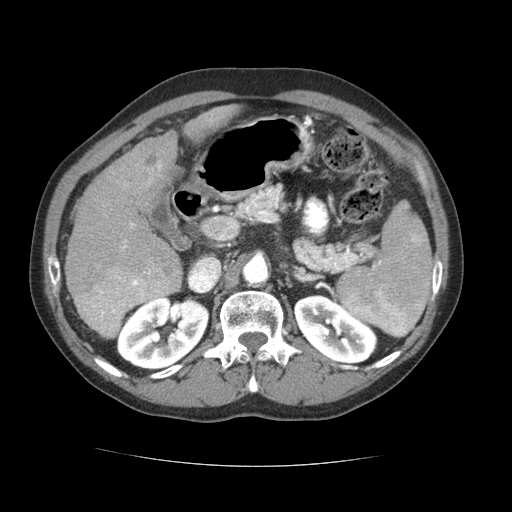
Contrast-enhanced abdominal CT (liver protocol), one axial slice. Position 38 of 69 along the scan axis. Reconstruction kernel STANDARD. 120 kVp. Soft-tissue window (W 400 / L 40 HU). 512 × 512 image matrix, field of view 360 × 360 mm. From the clinical record (not read from this slice): diagnosis: hepatocellular carcinoma (patient treated with transarterial chemoembolisation; whether this scan precedes or follows treatment is not stated here); TNM stage (as recorded): Stage-II; Child-Pugh class: B; tumour differentiation: poorly differentiated; tumour nodularity: multinodular.
Outlined on this slice (semi-automatically segmented with operator editing):
- liver parenchyma outside the tumour (the mass and vessels are separate outlines, so this box may not span the whole liver): bounding box [x1, y1, x2, y2] px = [64, 104, 240, 332]
- mass: [75, 266, 181, 339]
- liver vessels: [123, 164, 161, 273]